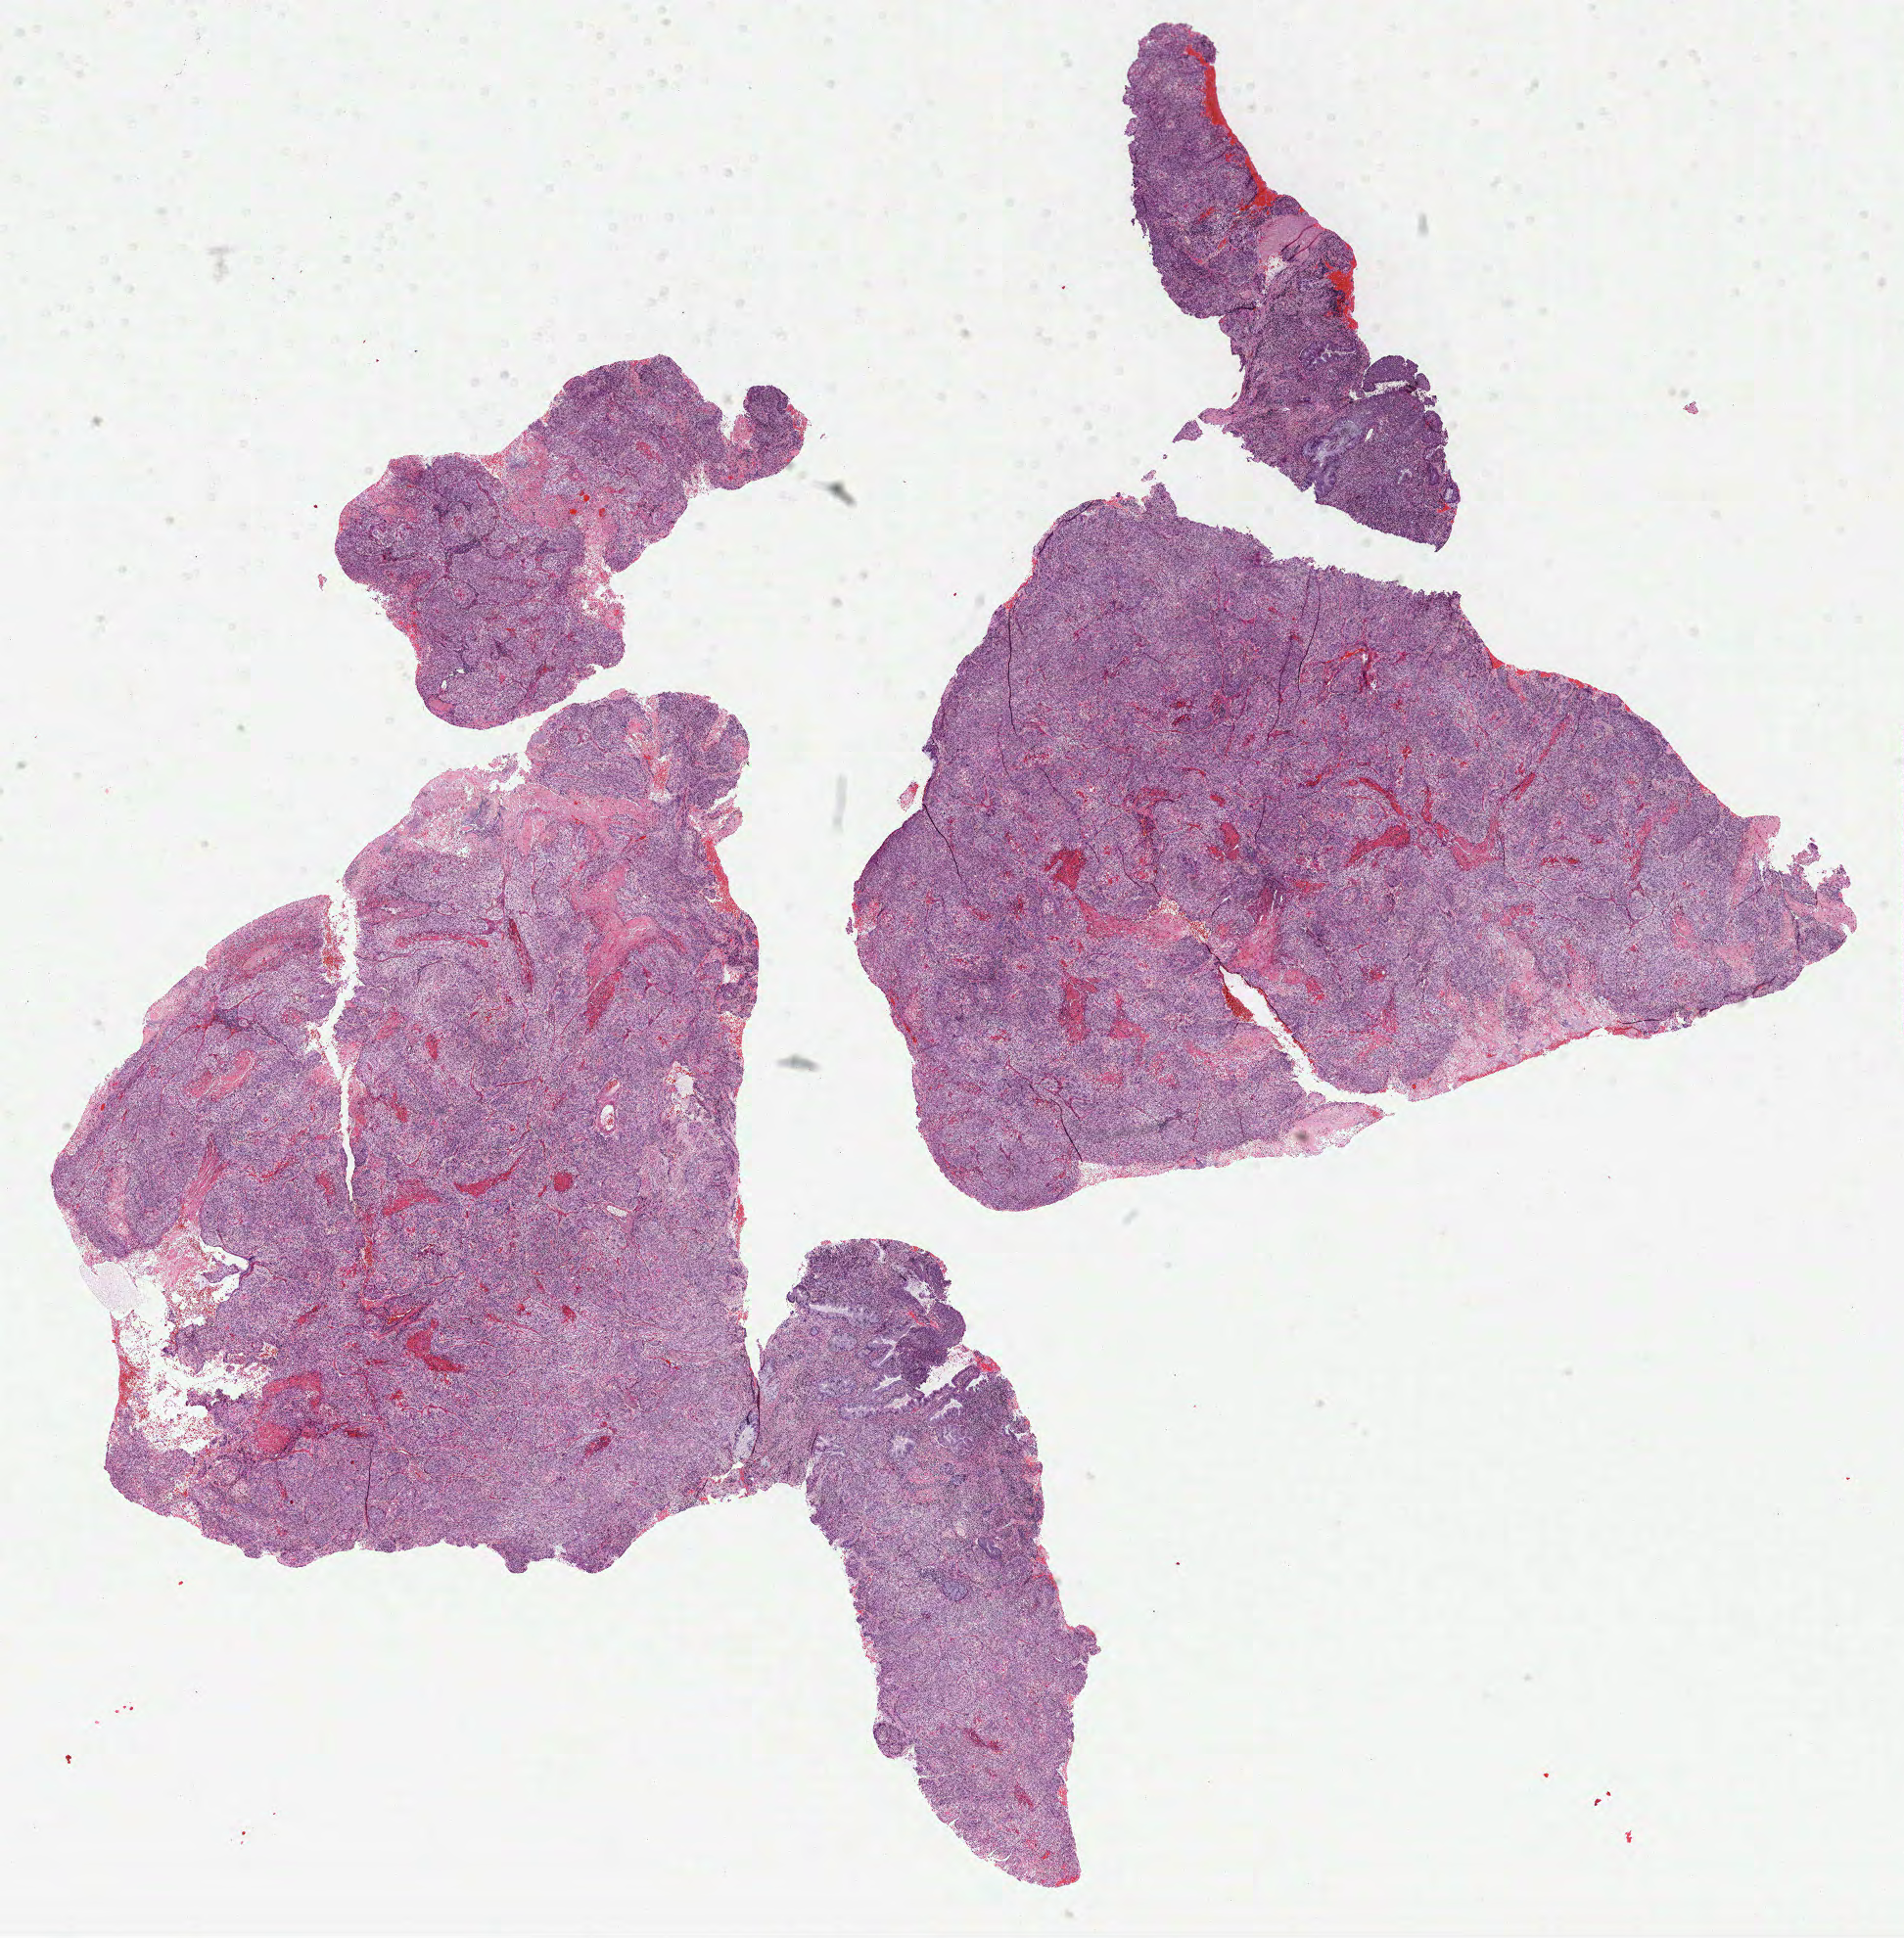
Whole-slide histology image, H&E-stained — whole scanned area (about 15.7 x 15.9 mm) shown as a low-resolution overview. Formalin-fixed paraffin-embedded (FFPE) diagnostic section. Sample: primary tumour, cervix. Female patient; age at initial diagnosis 25 years.
Diagnosis: Squamous cell carcinoma, keratinizing, NOS (cervix uteri).